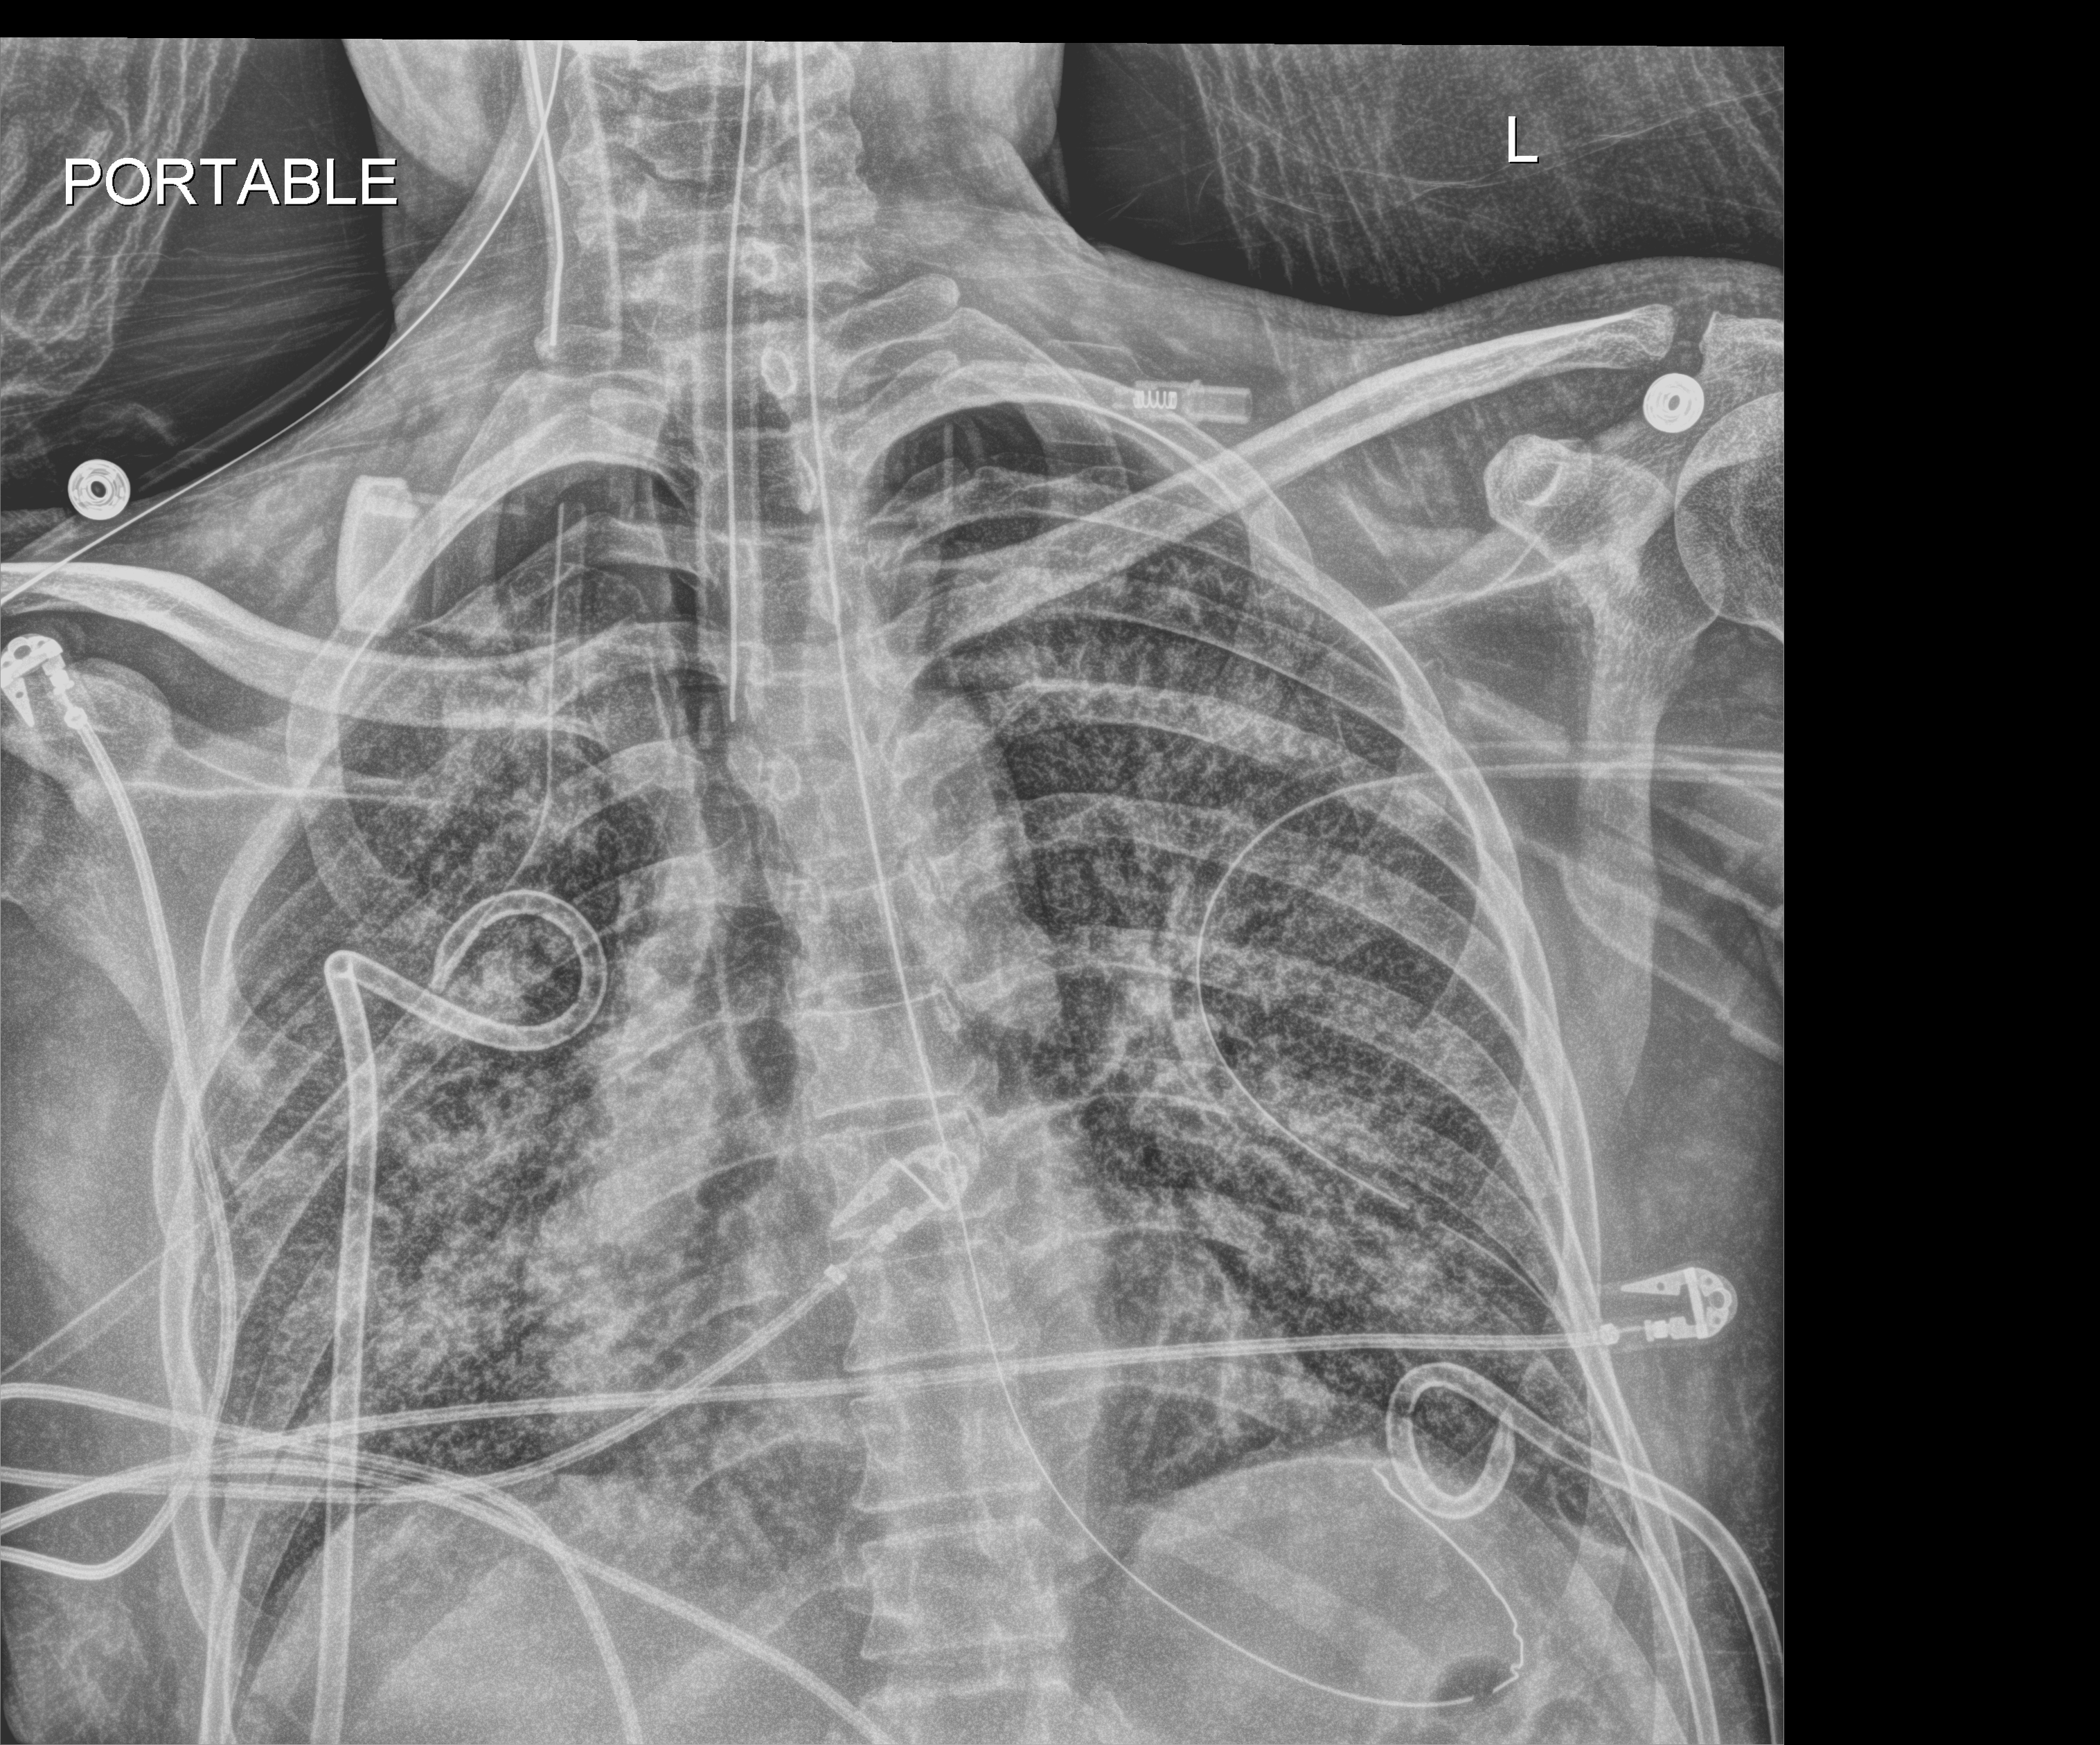
Chest X-ray (portable); anteroposterior (AP) projection. Patient hospitalised with COVID-19, aged 18–59 years.
From the hospital-stay record, not from the radiograph (when in the stay this image was taken is not recorded): length of hospital stay: 41 days; smoking status (admission record): never.